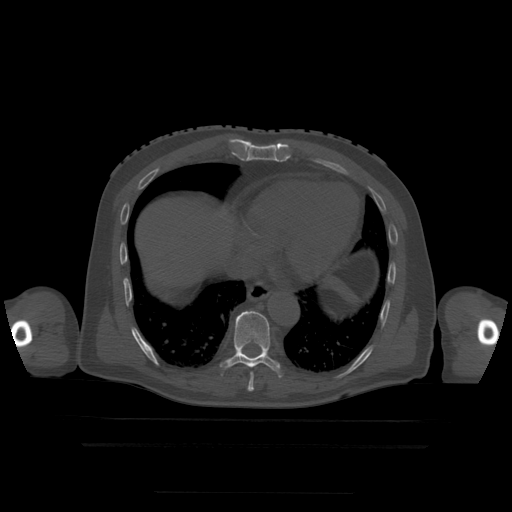
CT including the spine, one axial slice; position 262 of 522 along the scan axis; bone window (W 1800 / L 400 HU); 1.25 mm slice thickness; 512 × 512 image matrix, field of view 436 × 436 mm. Patient age 68 years. Case-level facts recorded for this patient, not image findings: primary cancer: urothelial.
Outlined on this slice (semi-automatically segmented with operator editing):
- T7 vertebra: bounding box <248,384,254,393> (left, top, right, bottom; pixels)
- T8 vertebra: <250,373,254,385>
- T9 vertebra: <221,311,282,378>